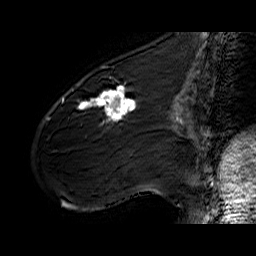
Breast MRI (dynamic contrast-enhanced), one sagittal slice; slice 20 of 60 in the series (ordered by position); dynamic contrast-enhanced series, time point 2 of 6 at this slice position (early post-contrast); 1.5 T; TE 6.4 ms, TR 32.9 ms; 4 mm slice thickness; 256 × 256 image matrix, field of view 200 × 200 mm. Female patient. From the clinical record (not read from this slice): setting: breast cancer imaged before/during neoadjuvant chemotherapy; receptor status: HER2-positive.
Outlined on this slice (semi-automatic segmentation, software-assisted and operator-edited):
- analysis volume of interest (the breast-tissue region the enhancement analysis was run in; not a lesion): bounding box [x1, y1, x2, y2] px = [61, 77, 141, 142]
- tumour enhancement mask (voxels above the 100 % enhancement threshold inside the analysis volume of interest): [62, 86, 138, 126]